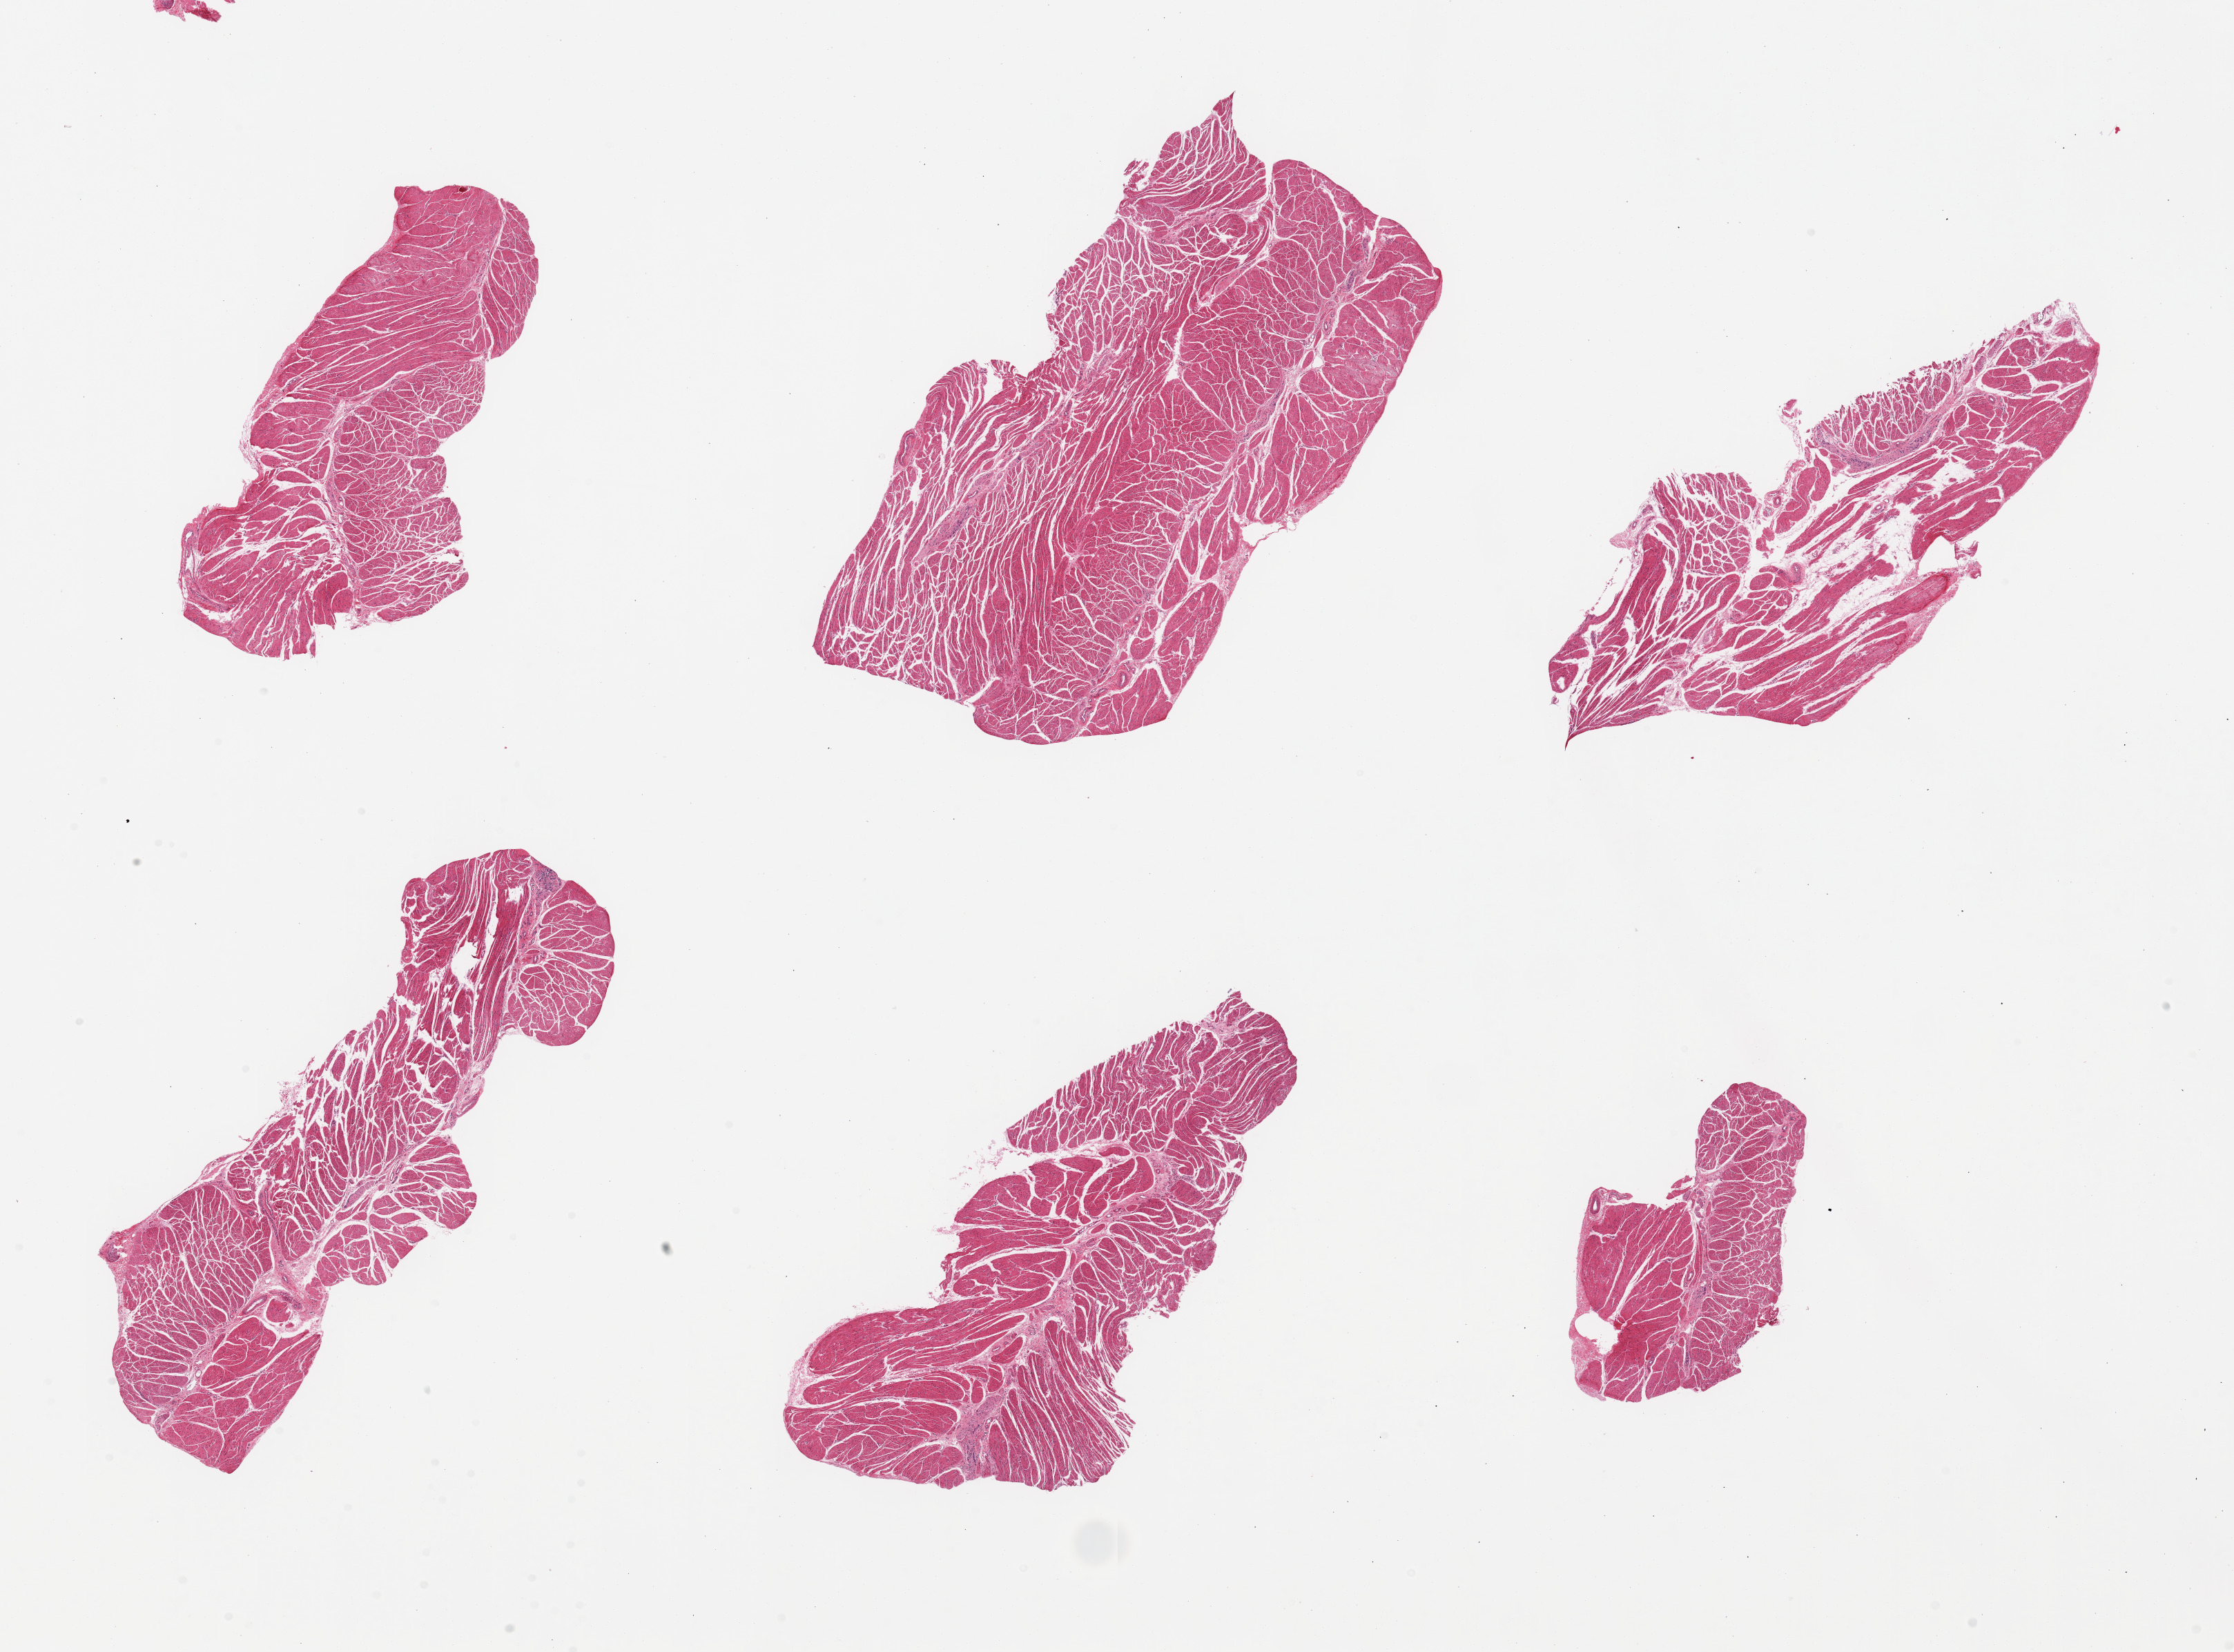
Whole-slide image, H&E stain, a low-resolution overview of the entire scanned area, about 25.6 x 18.9 mm. PAXgene-fixed, paraffin-embedded tissue. Sampled site (target tissue): esophageal muscle. Donor tissue sample. Donor sex: male.
• pathologist's review note for this sample: 6 pieces; target muscularis